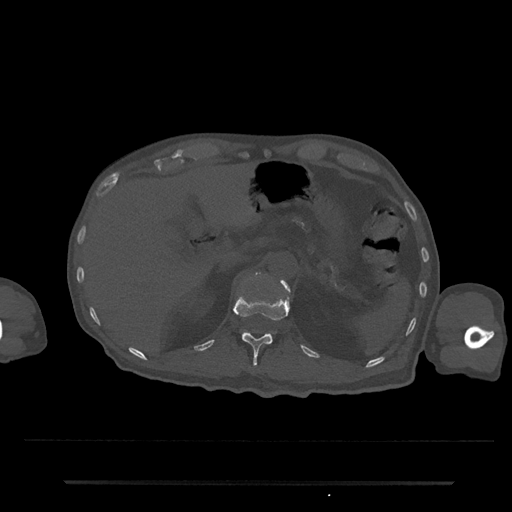
CT including the spine, one axial slice. Position 181 of 797 along the scan axis. 120 kVp. Bone window (W 1800 / L 400 HU). 0.5 mm slice thickness. 512 × 512 image matrix, field of view 427 × 427 mm. Male patient, age 74 years. Case-level facts recorded for this patient, not image findings: primary cancer: prostate.
Structures marked on this image (semi-automatically segmented with operator editing):
- L1 vertebra: box from (x=241, y=274) to (x=289, y=335) px
- T12 vertebra: (x=234, y=295)–(x=289, y=365)